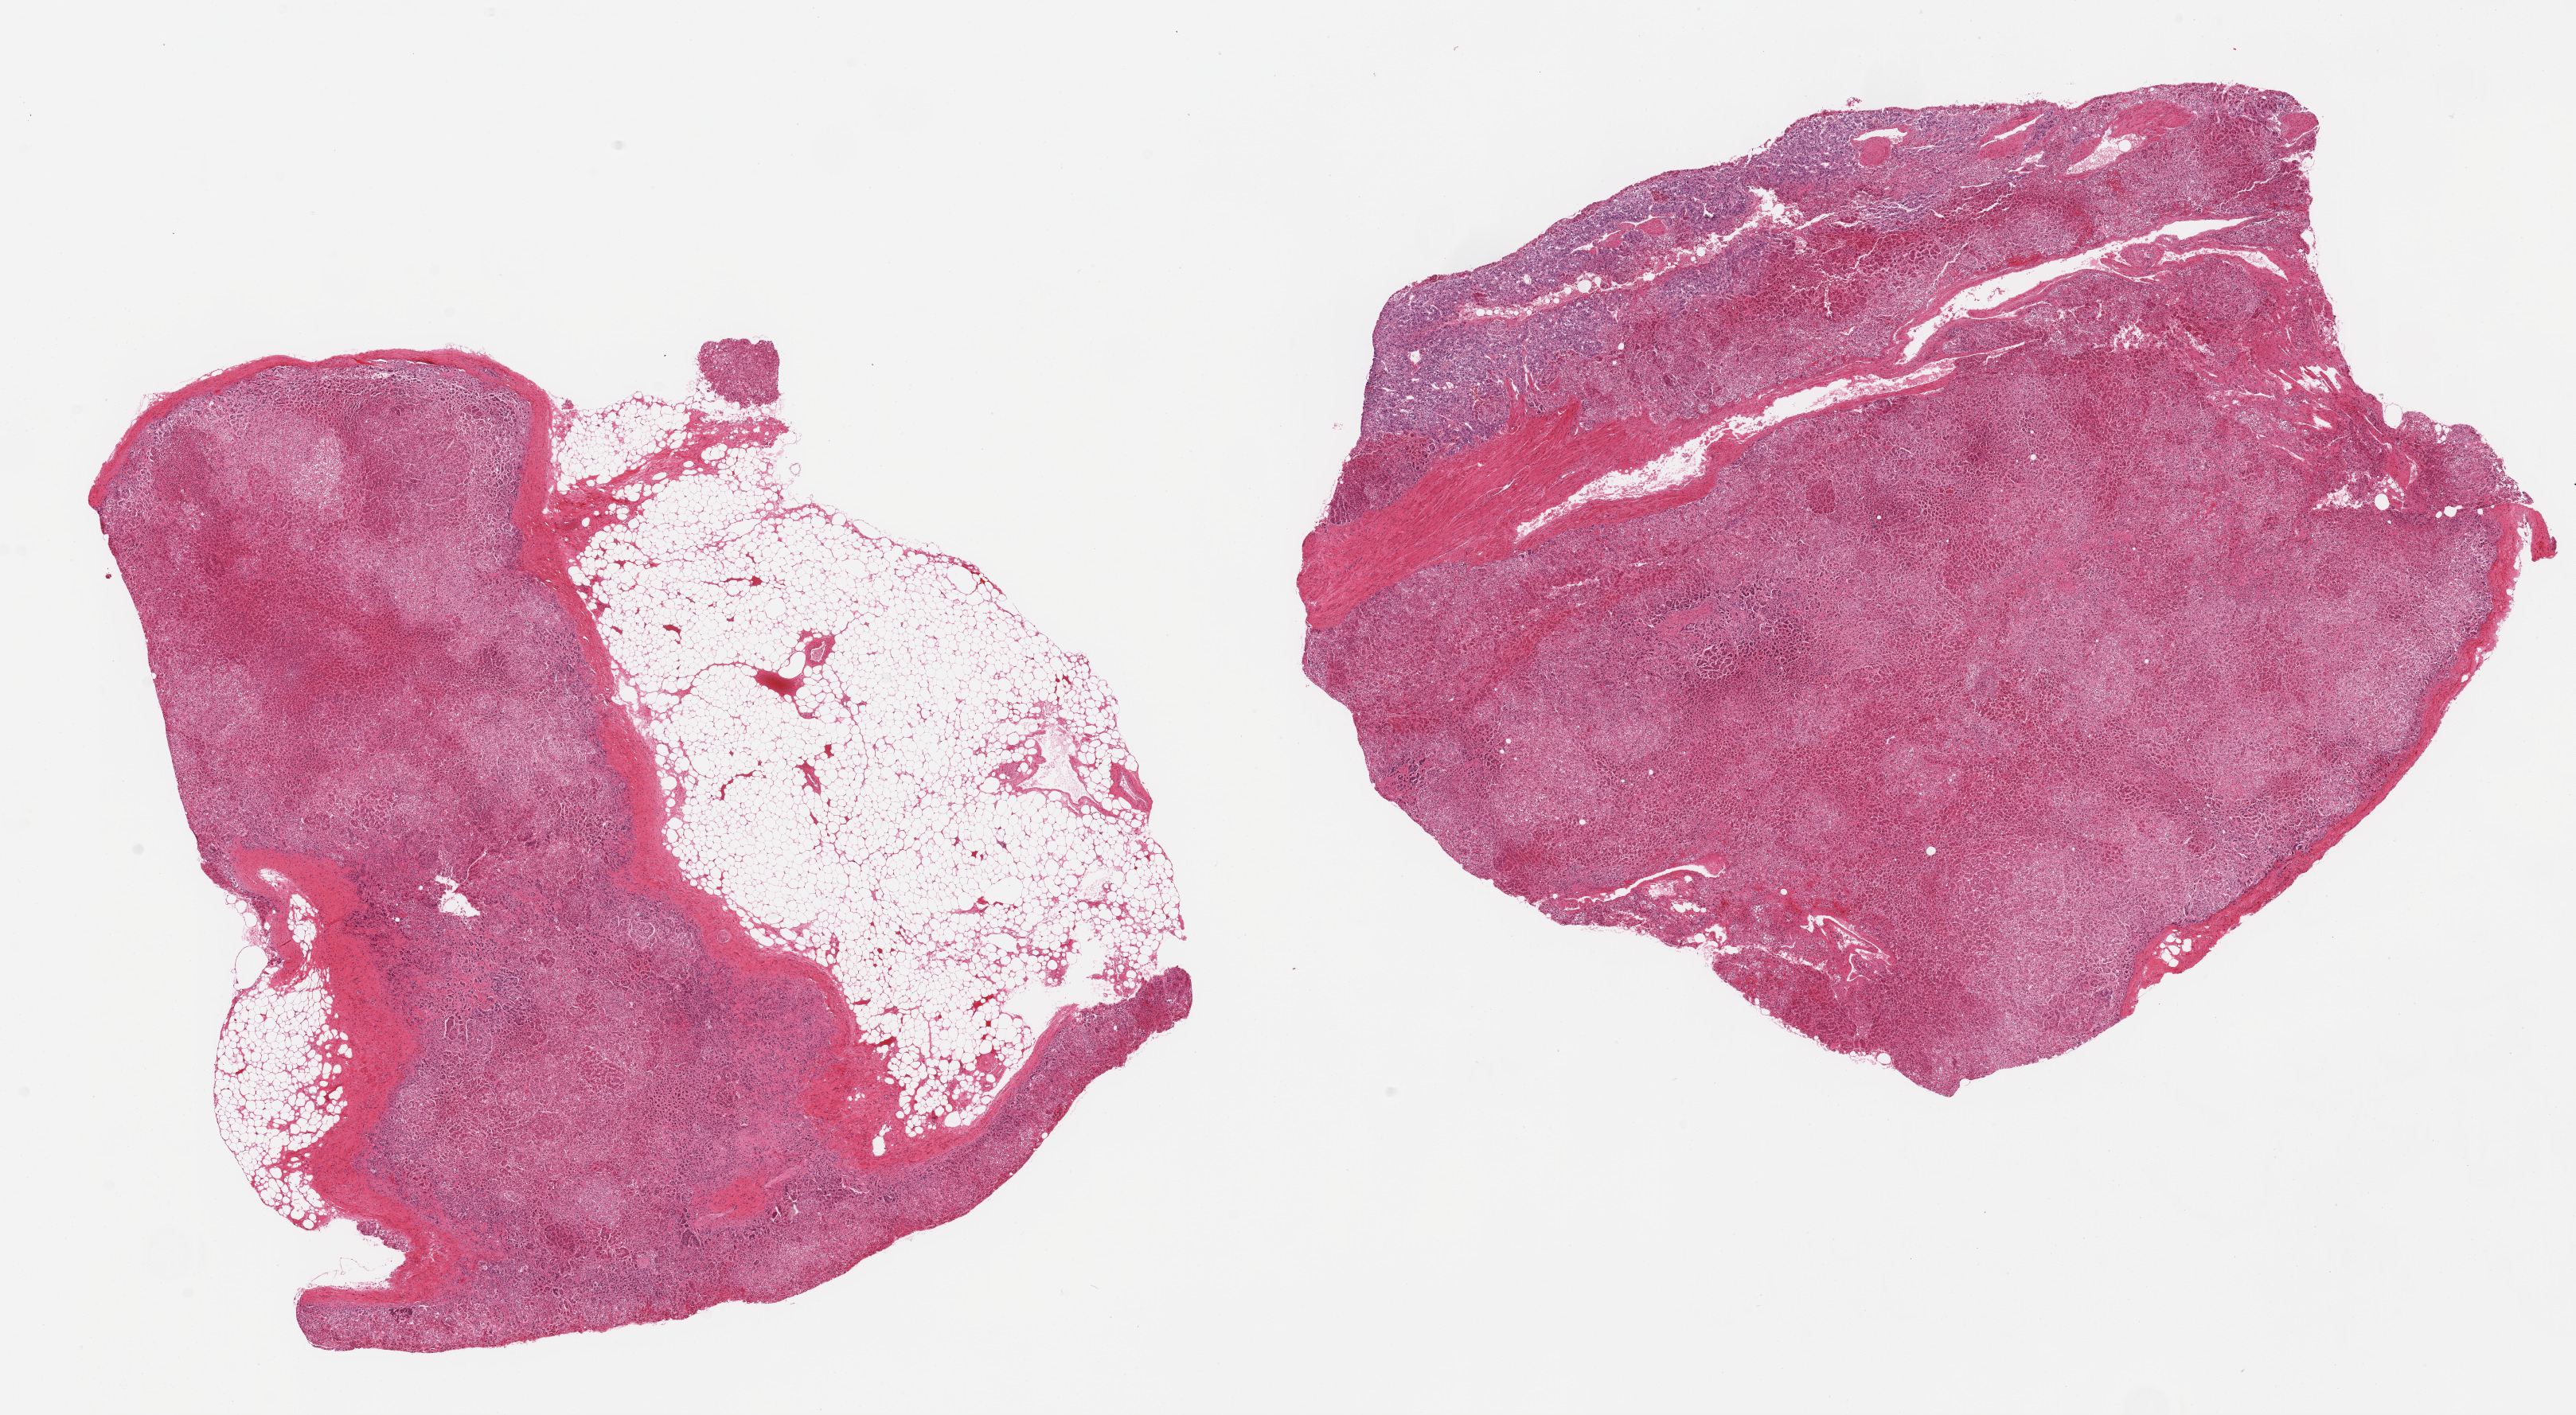
Whole-slide image, hematoxylin and eosin (H&E) stain, whole scanned area (about 25.6 x 14.1 mm, acquisition: 20x scan) shown as a low-resolution overview; PAXgene-fixed paraffin-embedded (PFPE) section; sampled site (target tissue): adrenal gland; donor tissue sample.
* pathologist's review note for this sample: 2 pieces; 40% external fat on 1 piece